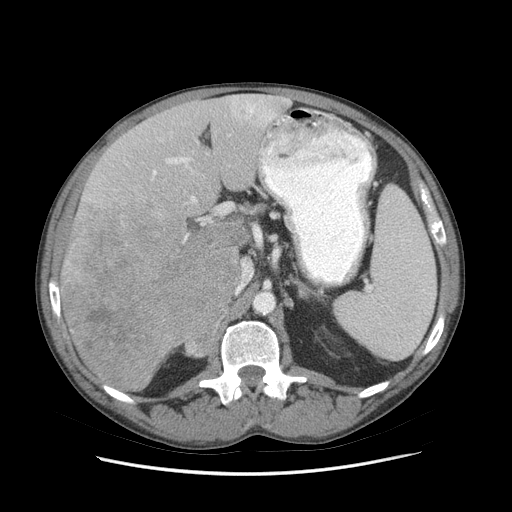
Contrast-enhanced abdominal CT (liver protocol), one axial slice; position 44 of 89 along the scan axis; soft-tissue window (W 400 / L 40 HU); 512 × 512 image matrix. From the clinical record (not read from this slice): diagnosis: hepatocellular carcinoma (patient treated with transarterial chemoembolisation; whether this scan precedes or follows treatment is not stated here); TNM stage (as recorded): Stage-IIIB; Child-Pugh class: A.
Annotated regions visible in this slice (semi-automatic segmentation, software-assisted and operator-edited):
- liver parenchyma outside the tumour (the mass and vessels are separate outlines, so this box may not span the whole liver): bounding box (x1, y1, x2, y2) in pixels: (58, 94, 288, 391)
- mass: (59, 208, 240, 389)
- liver vessels: (153, 97, 275, 202)